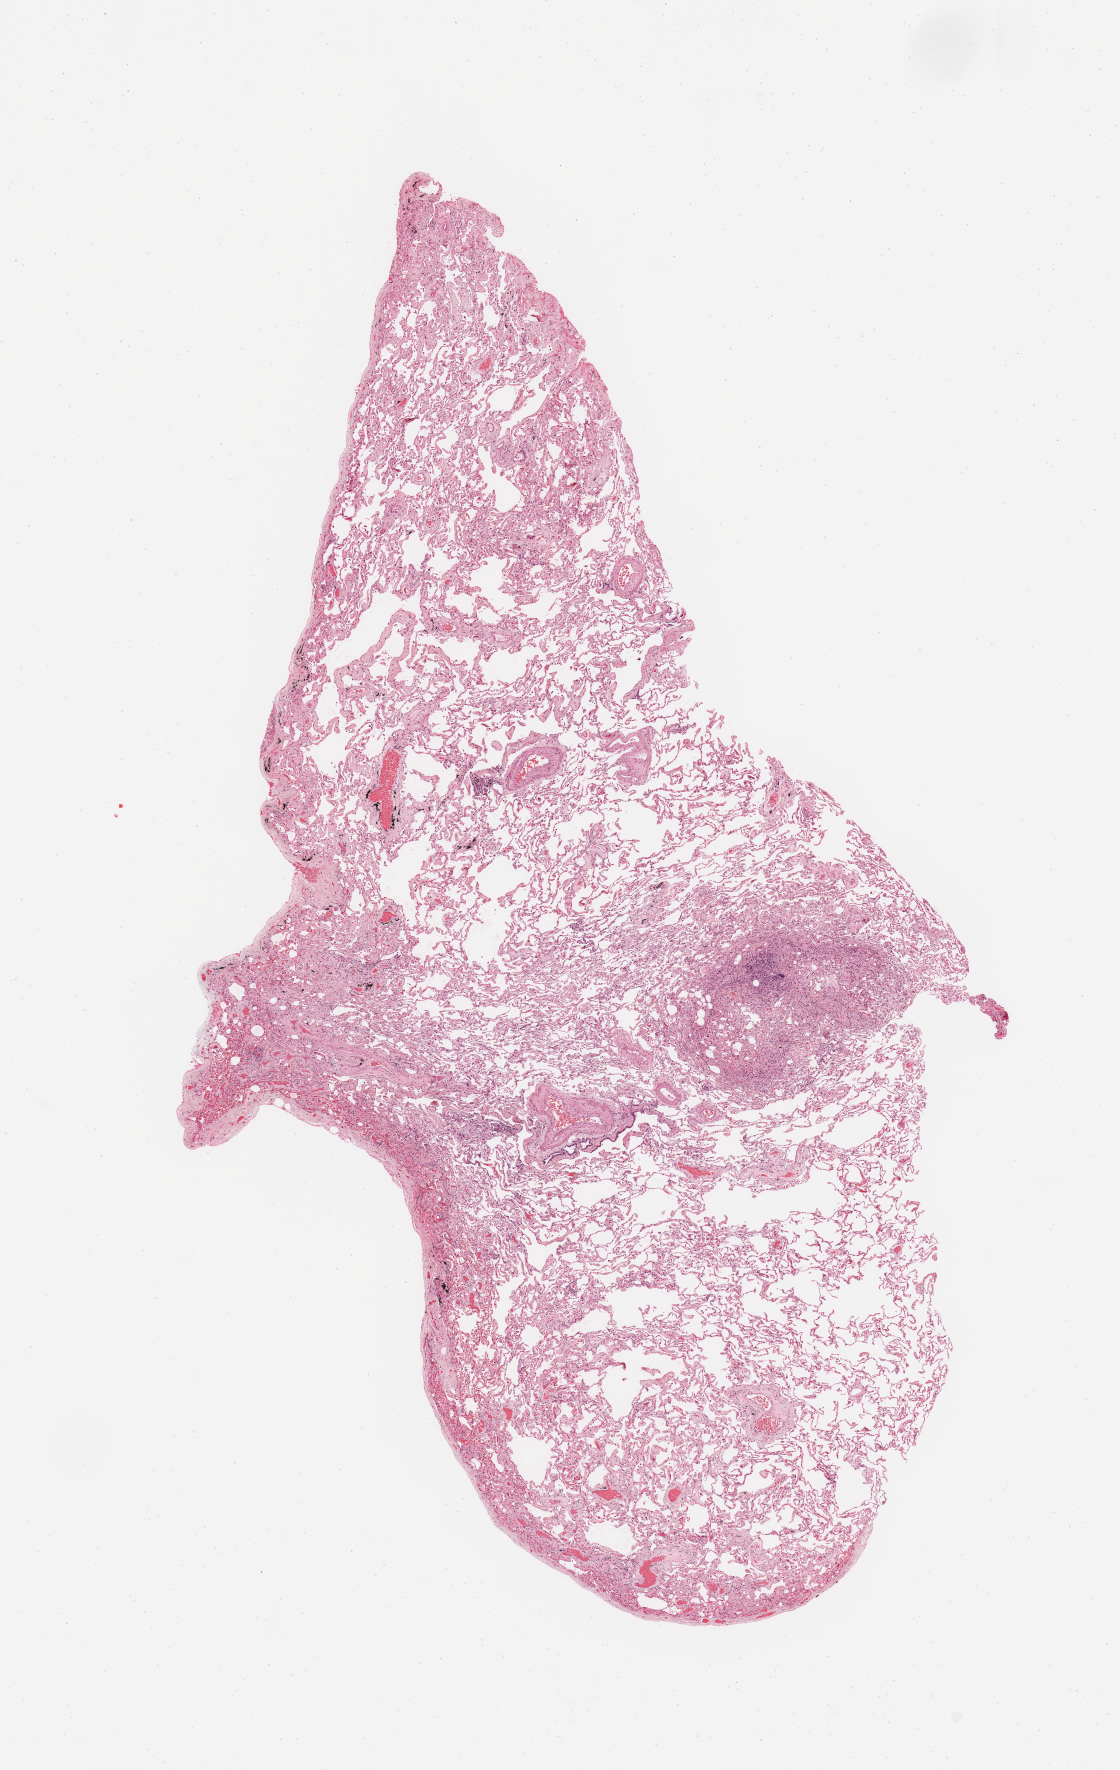
Whole-slide histology image, H&E — low-resolution overview of the scanned area, about 8.9 x 14.0 mm (slide scanned at 20x). Normal (non-tumour) tissue sample, sampled site: lung. 76-year-old male patient.
This section: normal (non-tumour) tissue from the same patient. Patient diagnosis: Squamous cell carcinoma, NOS.